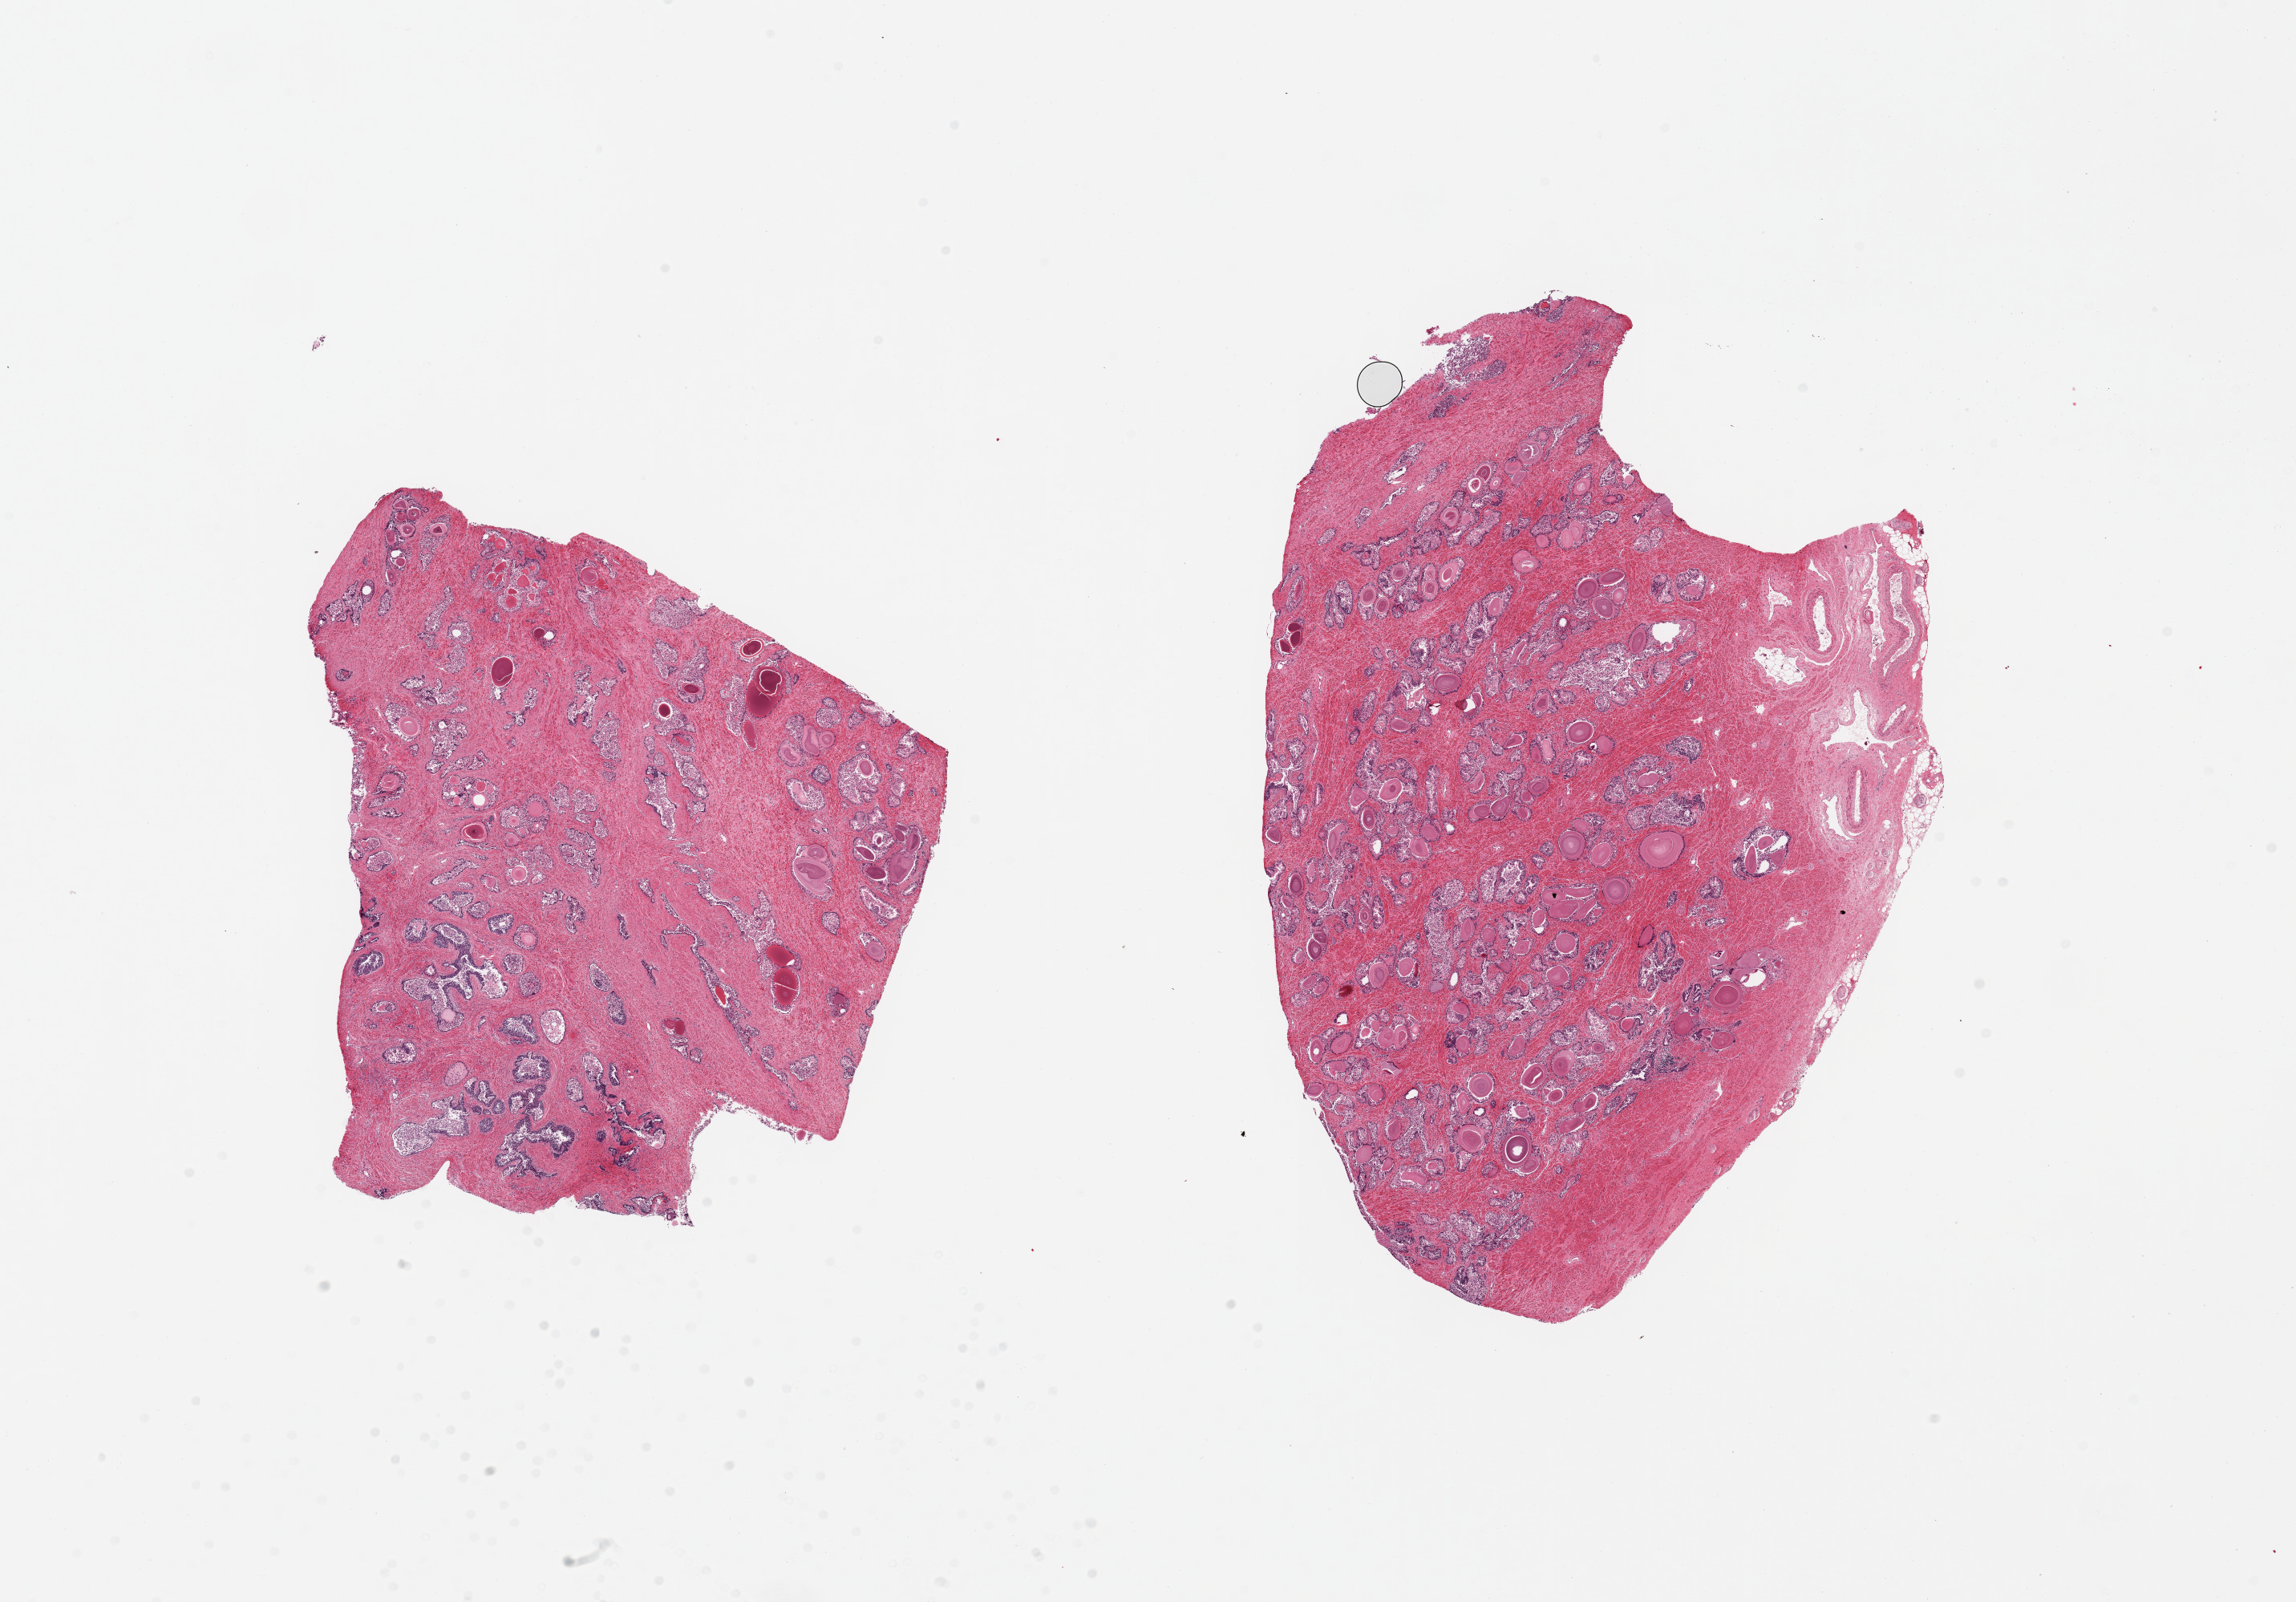
Digitized haematoxylin and eosin-stained section, a low-resolution overview of the entire scanned area, about 22.6 x 15.8 mm (slide scanned at 20x). PAXgene-fixed, paraffin-embedded tissue. Sampled site (target tissue): prostate. Donor tissue sample. Donor sex: male.
Reviewer comment on this tissue sample: 2 pieces, hyperplastic glandular pattern; glandular mucosal cells moderately-markedly autolyzed.